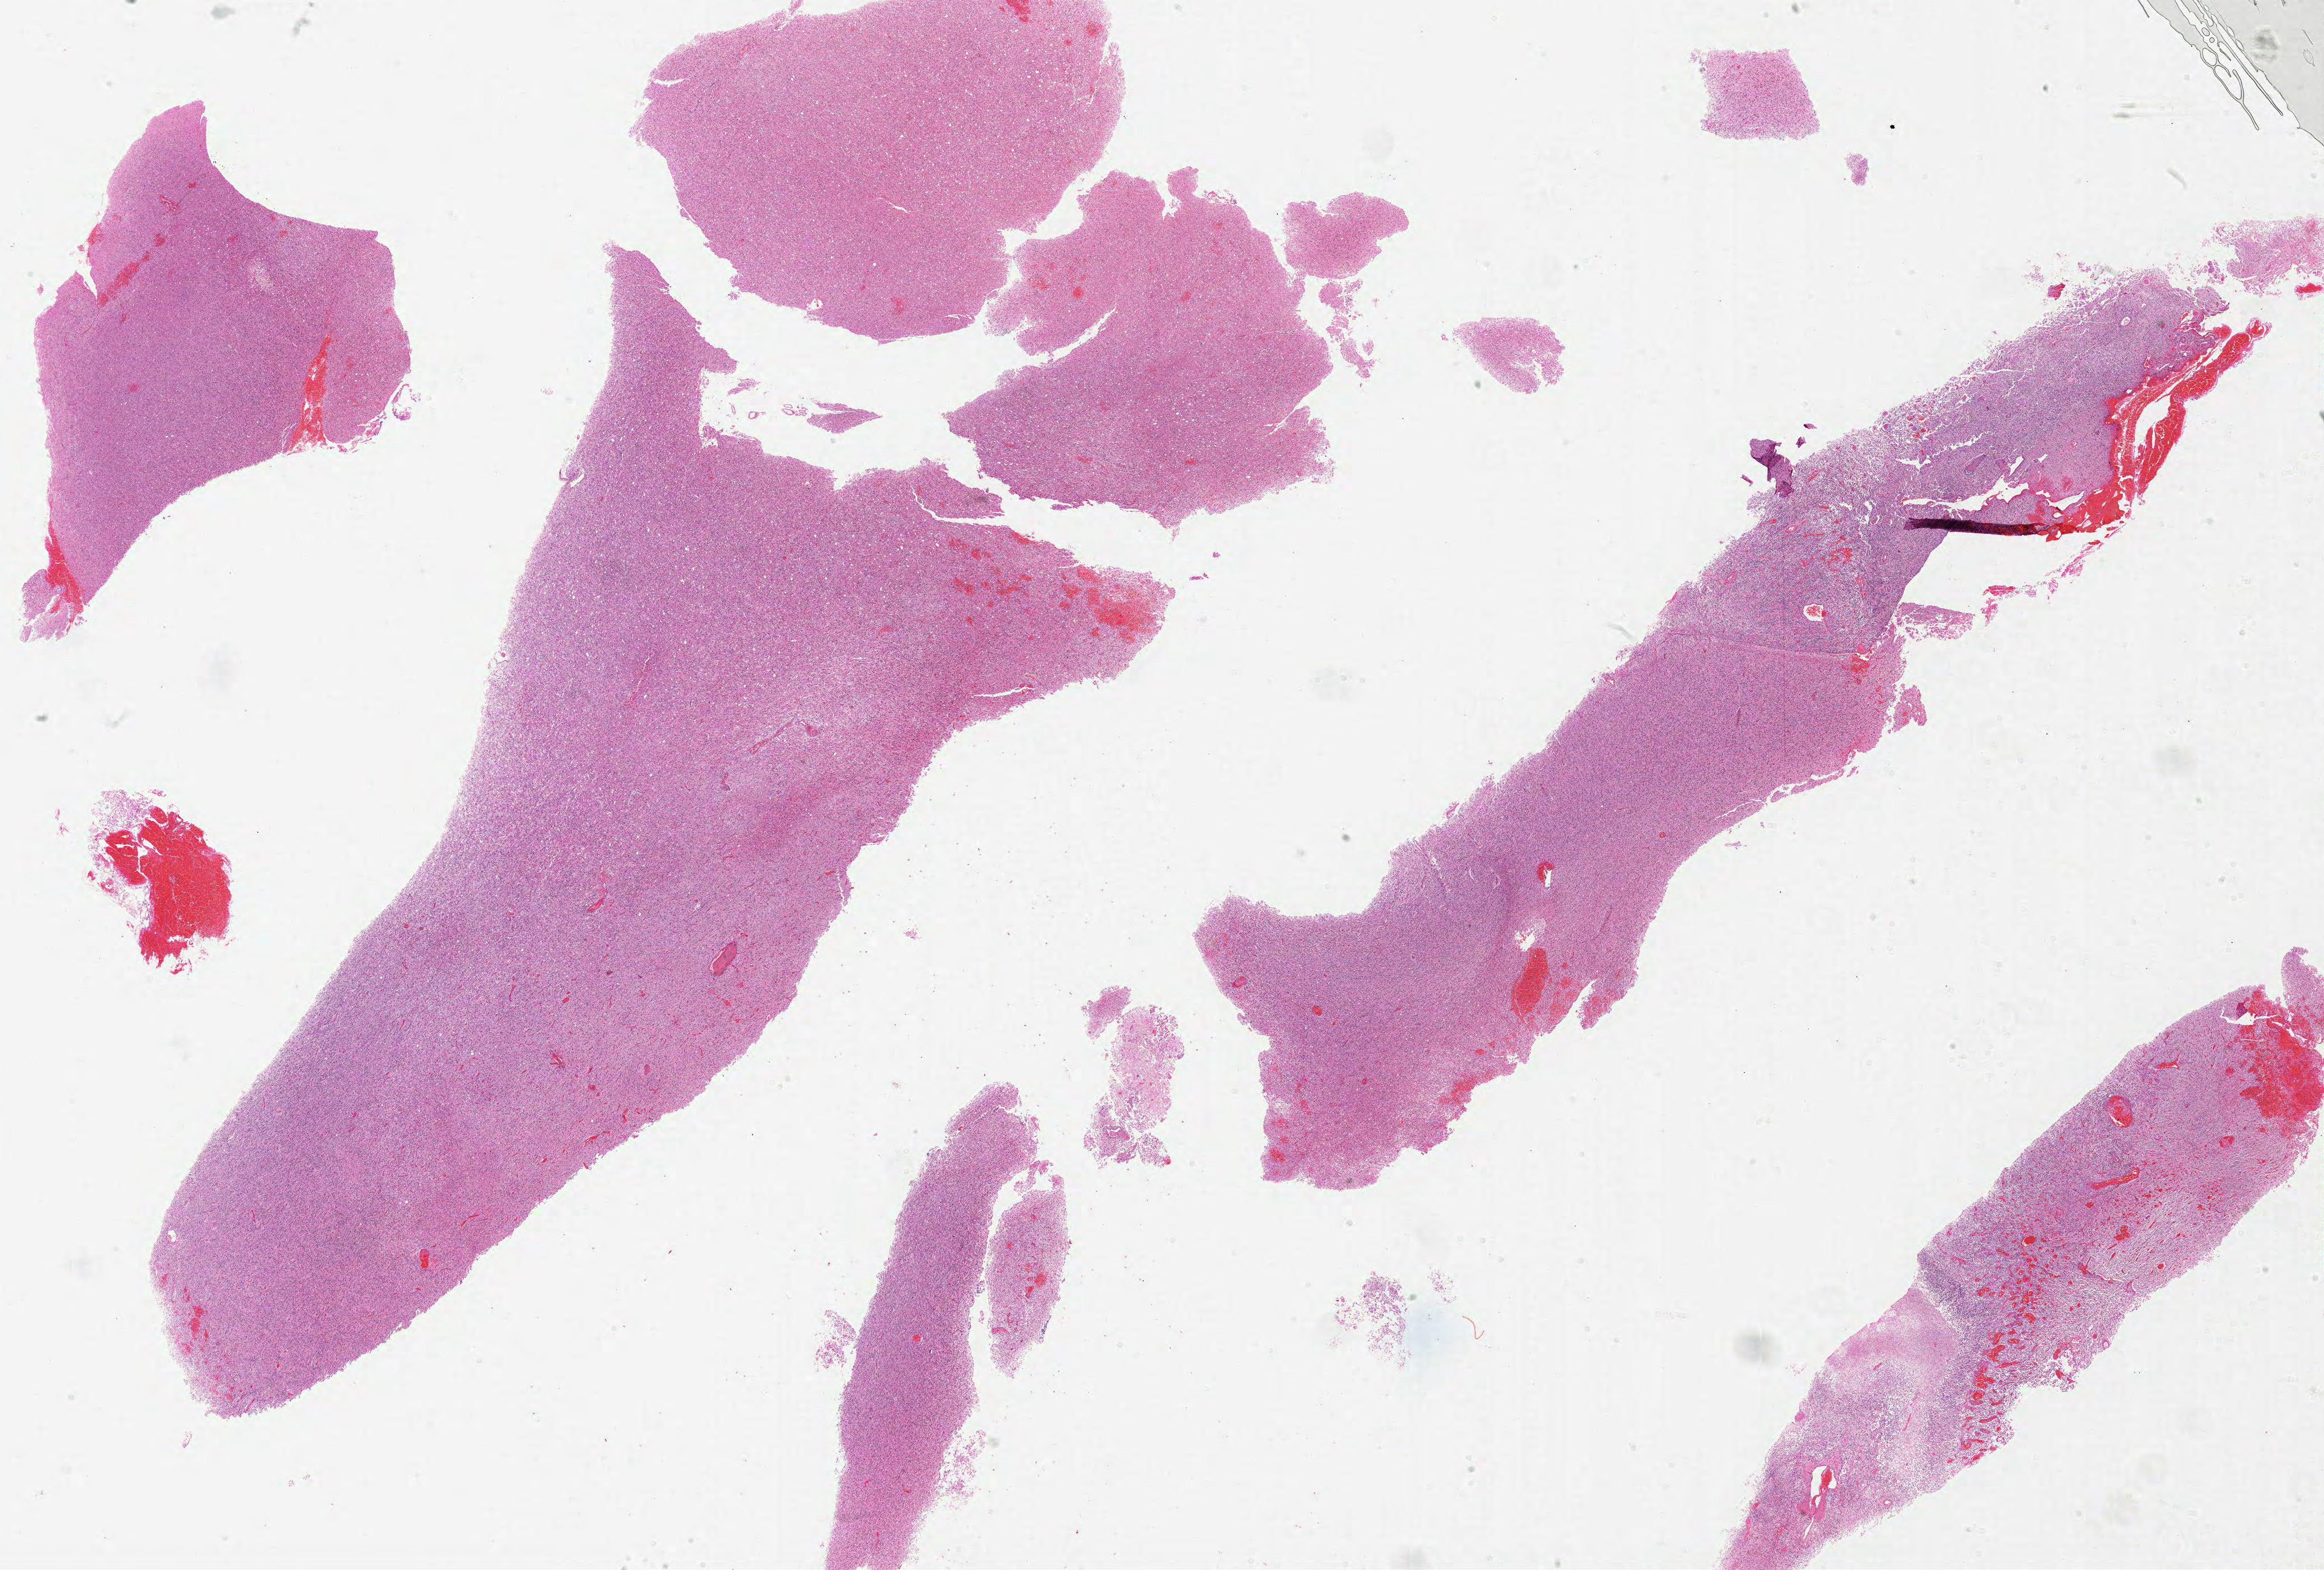
Digitized Hematoxylin and eosin (H&E) stained tissue section (whole slide), shown as a low-resolution overview of the whole scanned area (about 33.0 x 22.3 mm, from a 20x scan), formalin-fixed paraffin-embedded (FFPE) diagnostic section, sample: primary tumour, brain. Female patient; age at initial diagnosis 48 years.
• diagnosis: Glioblastoma